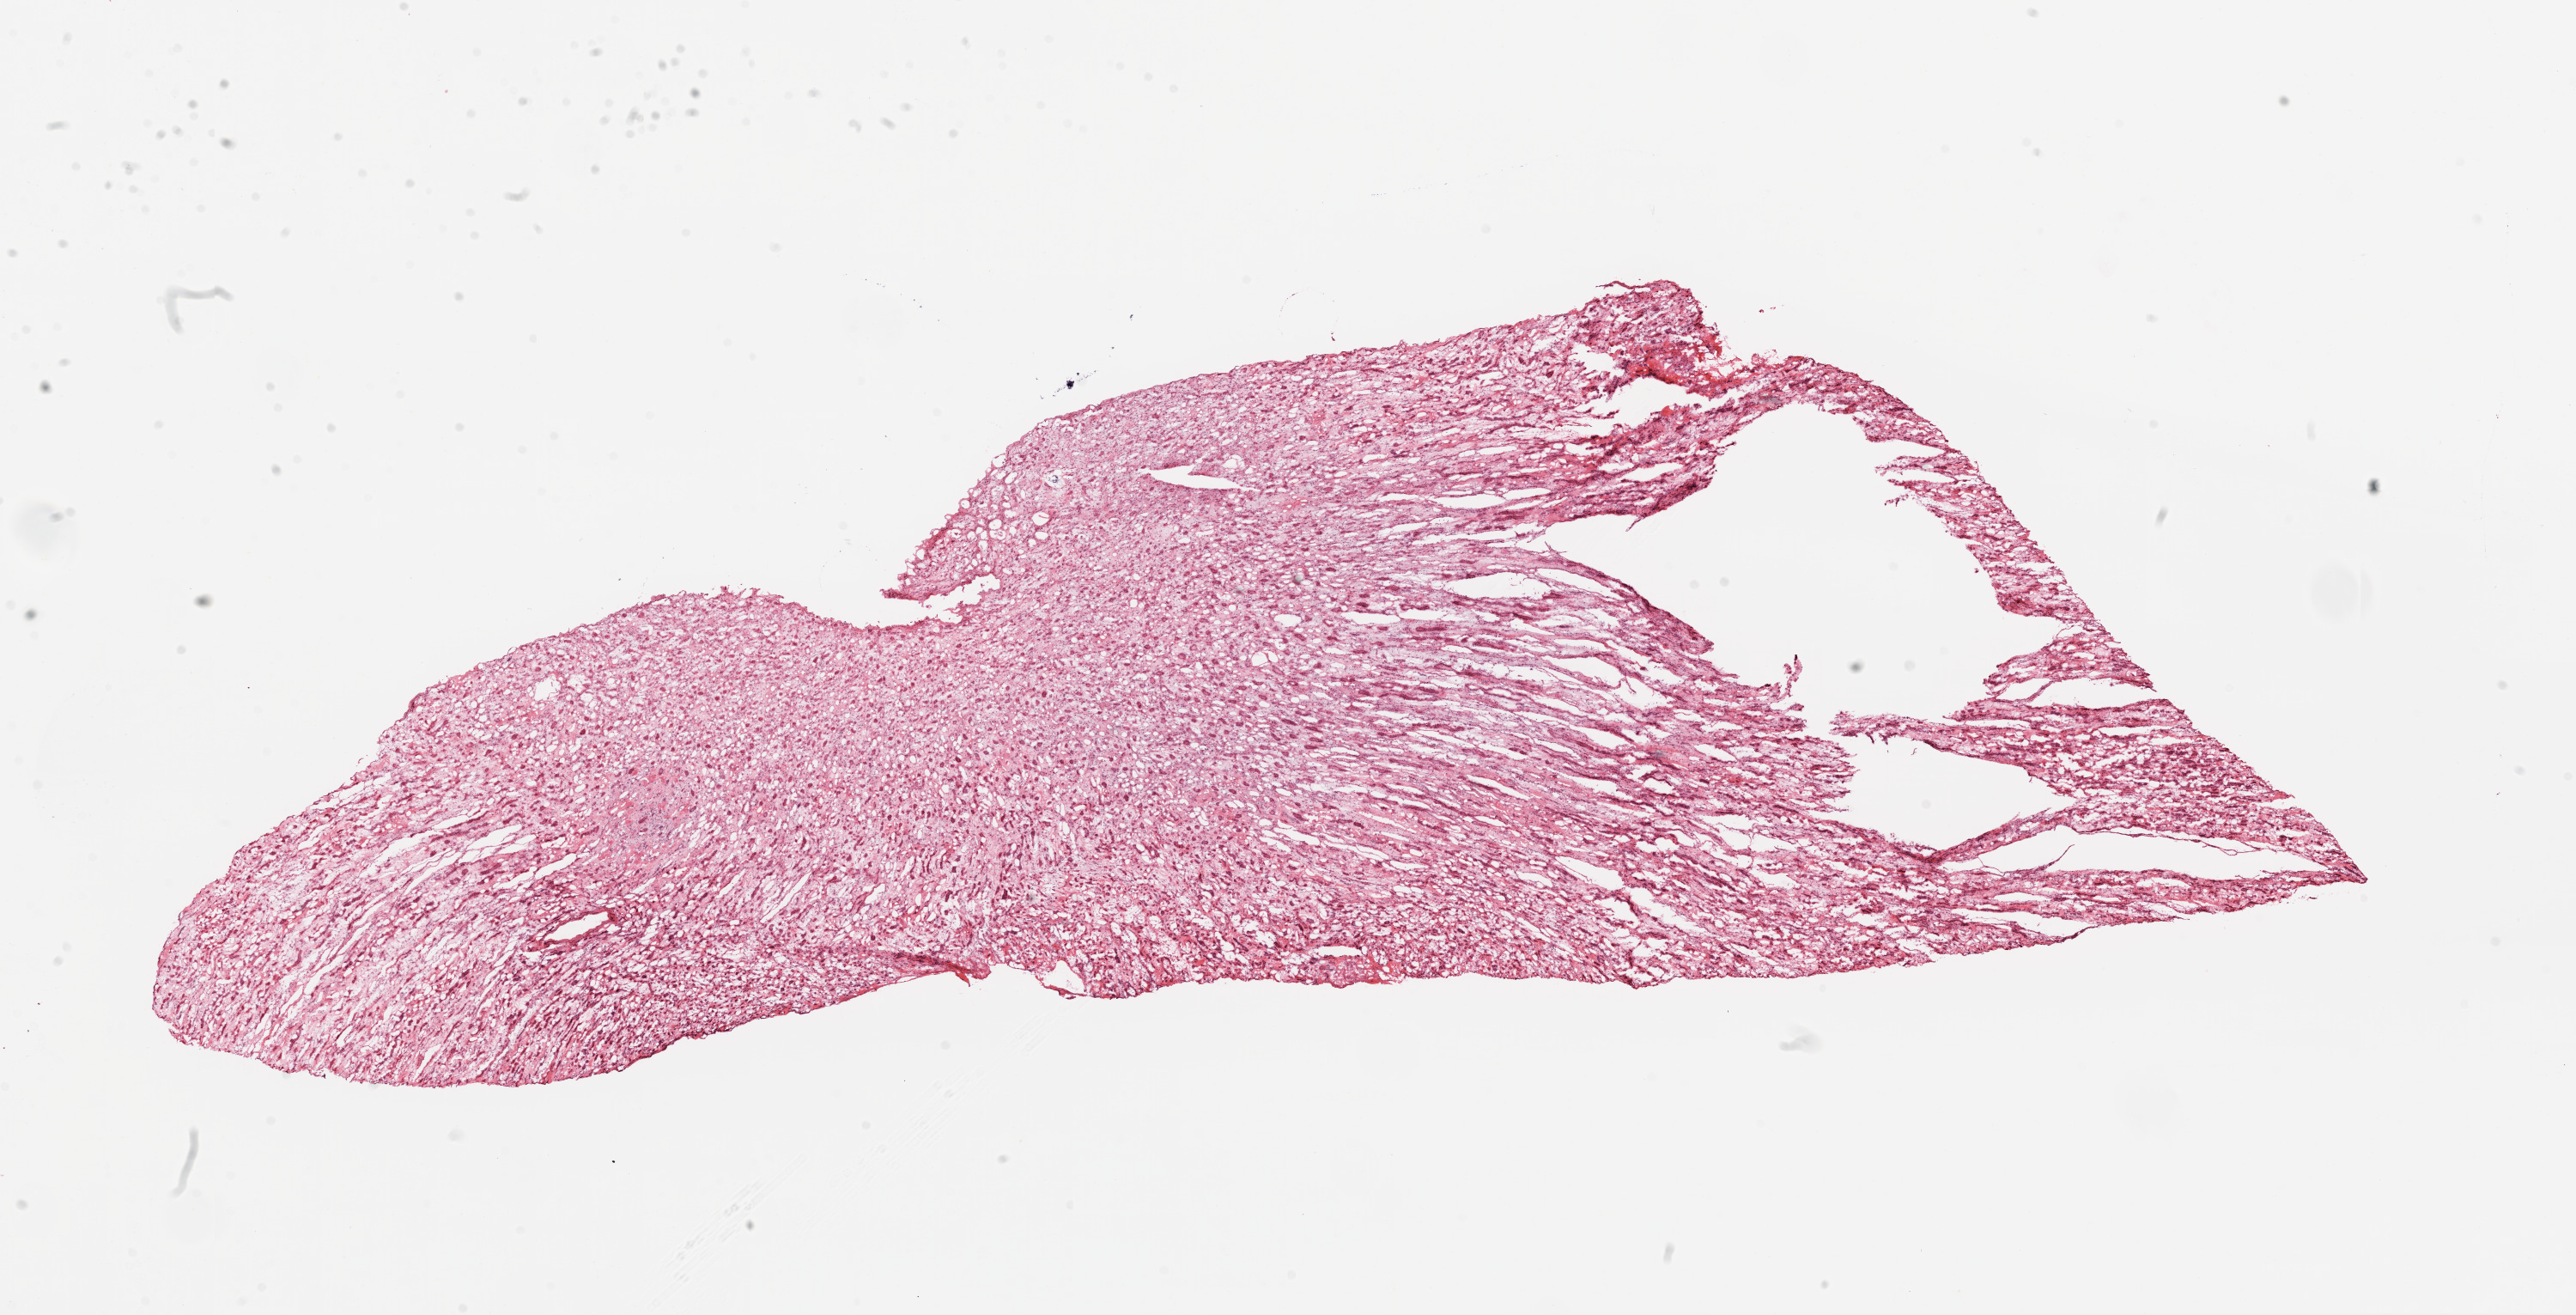
Whole-slide histology image, H&E — shown as a low-resolution overview of the whole scanned area (about 24.1 x 12.3 mm, from a 20x scan); frozen section from the top of the tissue portion; sample: solid tissue normal (non-tumour tissue), kidney. Patient: female, age at initial diagnosis 76 years.
This section: solid tissue normal (non-tumour) sample from the same patient. Patient diagnosis: Clear cell adenocarcinoma, NOS.